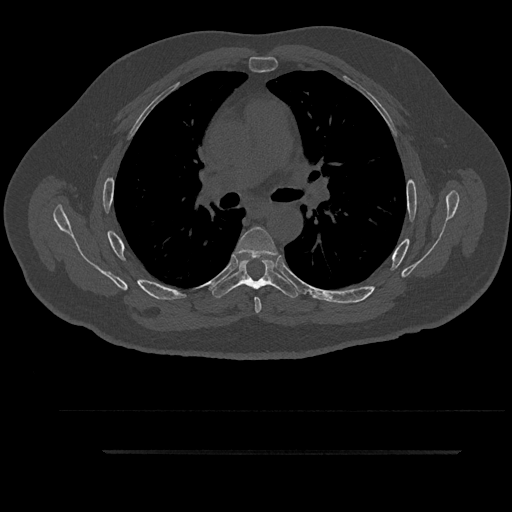
CT including the spine, one axial slice; position 600 of 797 along the scan axis; reconstruction kernel Br40s/3; 120 kVp; bone window (W 1800 / L 400 HU); 512 × 512 image matrix, field of view 432 × 432 mm. Patient: male, 63 years. From the clinical record (not read from this slice): primary cancer: renal.
Structures marked on this image (semi-automatic segmentation, software-assisted and operator-edited):
- T5 vertebra: bounding box [x1, y1, x2, y2] px = [234, 227, 279, 313]
- T6 vertebra: [211, 256, 300, 298]